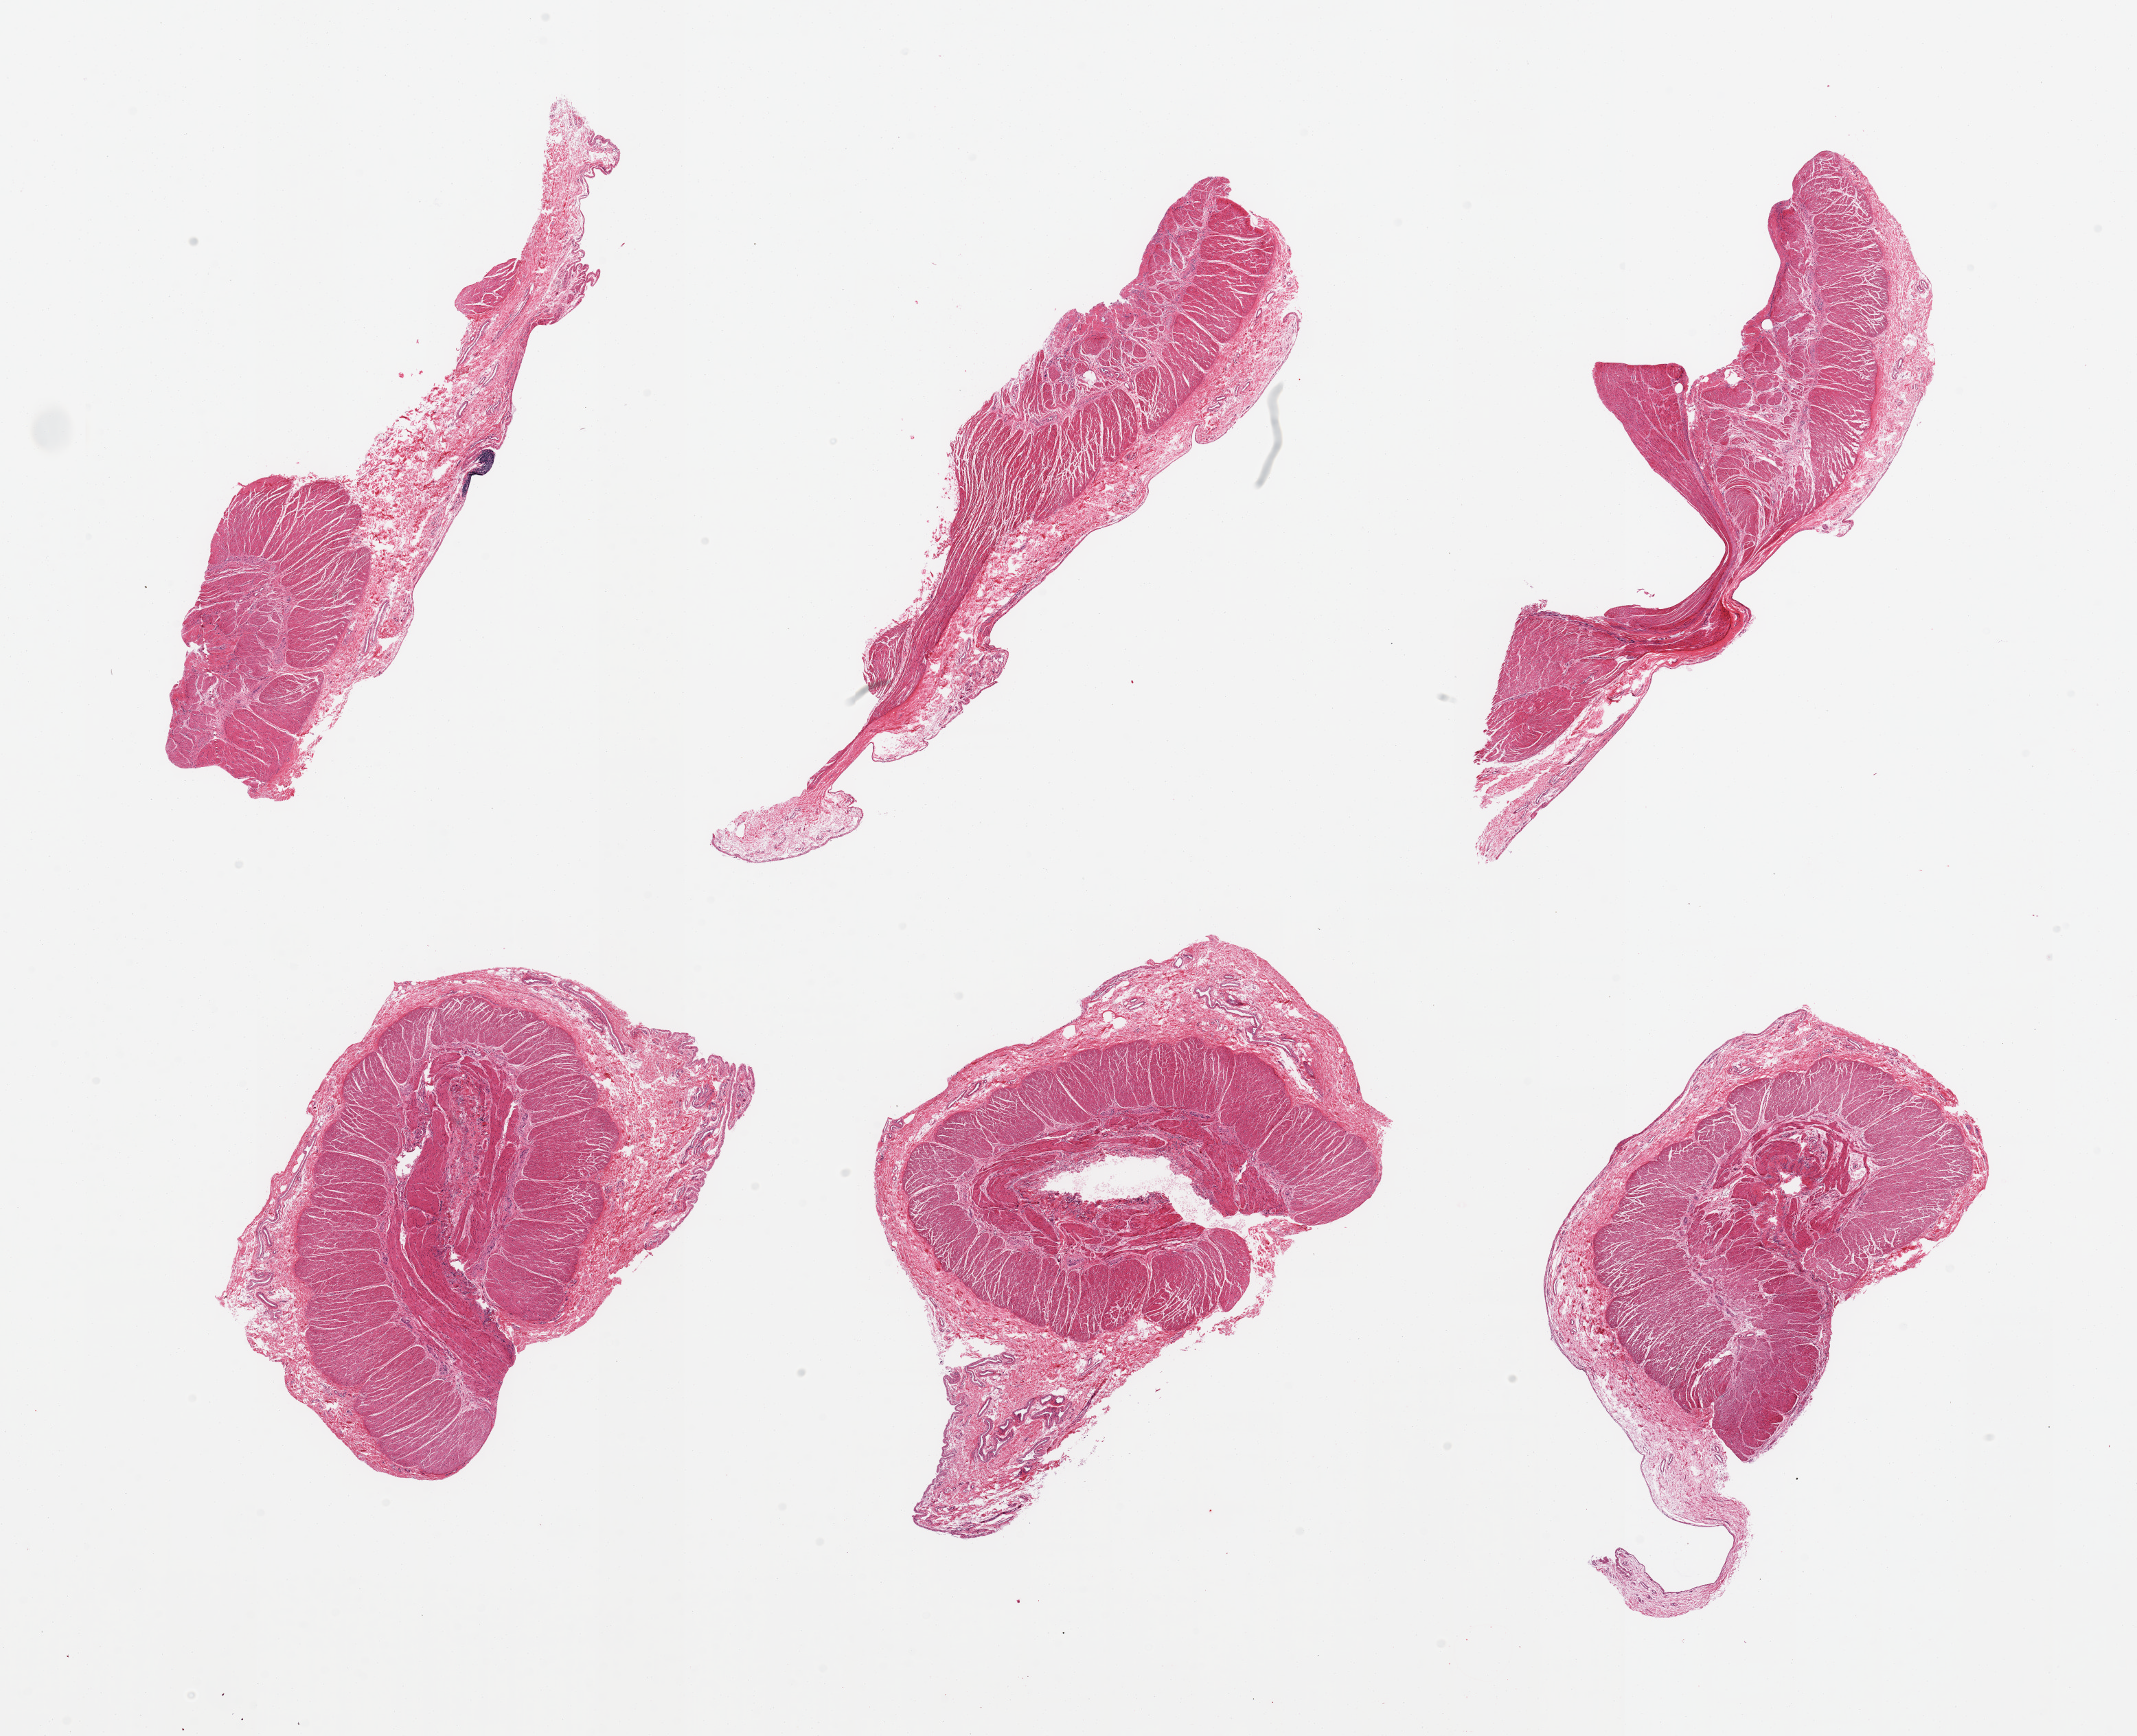
Whole-slide image, hematoxylin and eosin (H&E) stain, brightfield, a low-resolution overview of the entire scanned area, about 24.6 x 20.0 mm (acquisition: 20x scan), PAXgene-fixed, paraffin-embedded tissue, sampled site (target tissue): sigmoid colon, donor tissue sample. Male donor.
Reviewer comment on this tissue sample: 6 pieces, confirmed target muscularis.